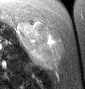
MRI of an extremity soft-tissue mass, one axial slice. Position 23 of 46 along the scan axis. T2-weighted fat-saturated. MR volume resampled by the dataset authors to the PET/CT grid (not the native acquisition matrix). 3.27 mm slice thickness. 85 × 89 image matrix, field of view 83 × 87 mm. Female patient. Case-level facts recorded for this patient, not image findings: histological type: leiomyosarcoma; grade: intermediate; site of the primary tumour: parascapusular.
Outlined on this slice (expert contour drawn on MRI and transferred to this co-registered scan by the dataset authors):
- gross tumour volume including surrounding oedema: bounding box [x1, y1, x2, y2] px = [16, 21, 60, 67]
- gross tumour volume (mass): [18, 21, 55, 65]